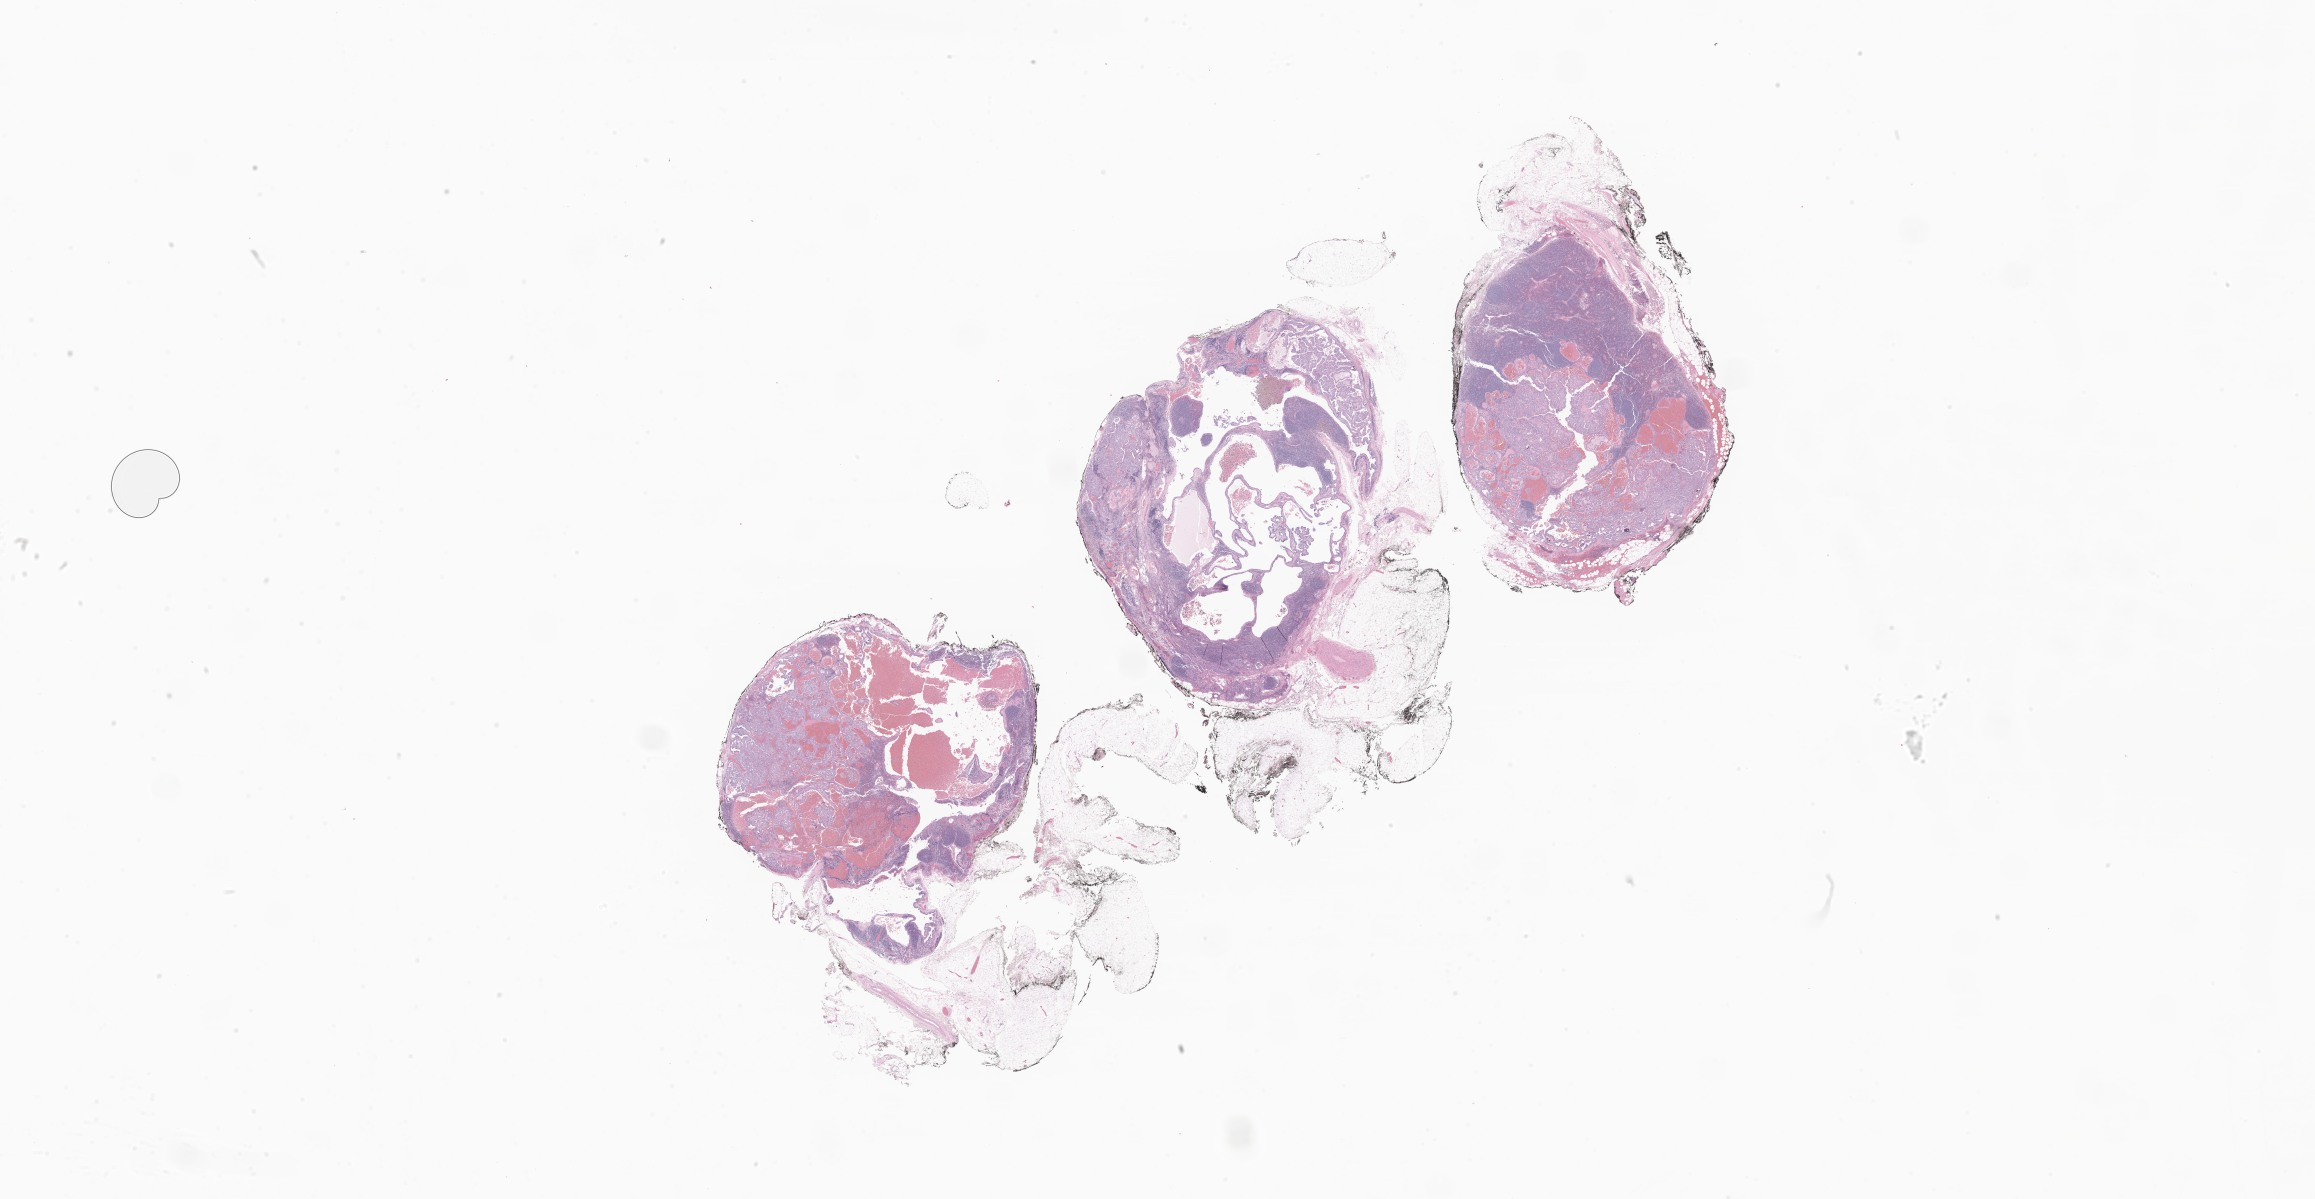
Whole-slide image, H&E stain of tumor tissue from the thyroid, whole scanned area (about 39.1 x 20.2 mm) shown as a low-resolution overview; formalin-fixed paraffin-embedded section. Patient: female, age 205 months (17 years 1 month).
Recorded diagnosis: Papillary carcinoma, NOS.